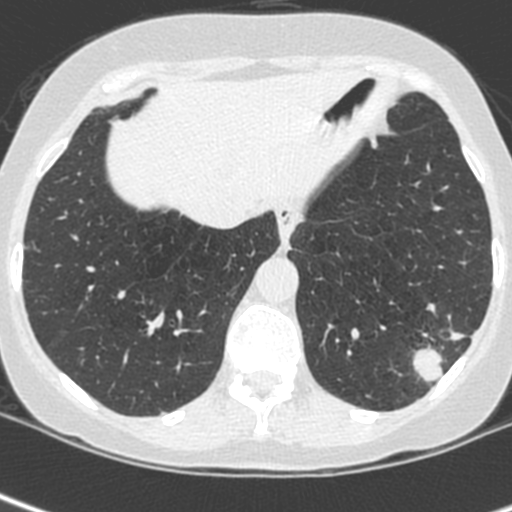
Chest CT (low-dose screening protocol), one axial image, first (baseline) screen, lung window (W 1500 / L -600 HU), slice 183 of 252 in the series. Female participant, aged 56 years at enrolment.
Lesion marked by an expert reader, box from (x=399, y=302) to (x=481, y=386) px. Screening reader's record for this exam (one nodule recorded; not confirmed to be the boxed lesion): non-calcified nodule or mass ≥4 mm, left lower lobe, 37 × 29 mm, spiculated (stellate) margins, ground glass attenuation. Participant outcome: lung cancer diagnosed 91 days after this screen — squamous cell carcinoma, NOS, left lower lobe, poorly differentiated (G3), stage IIIA (AJCC 6th edition), 35 mm at pathology.